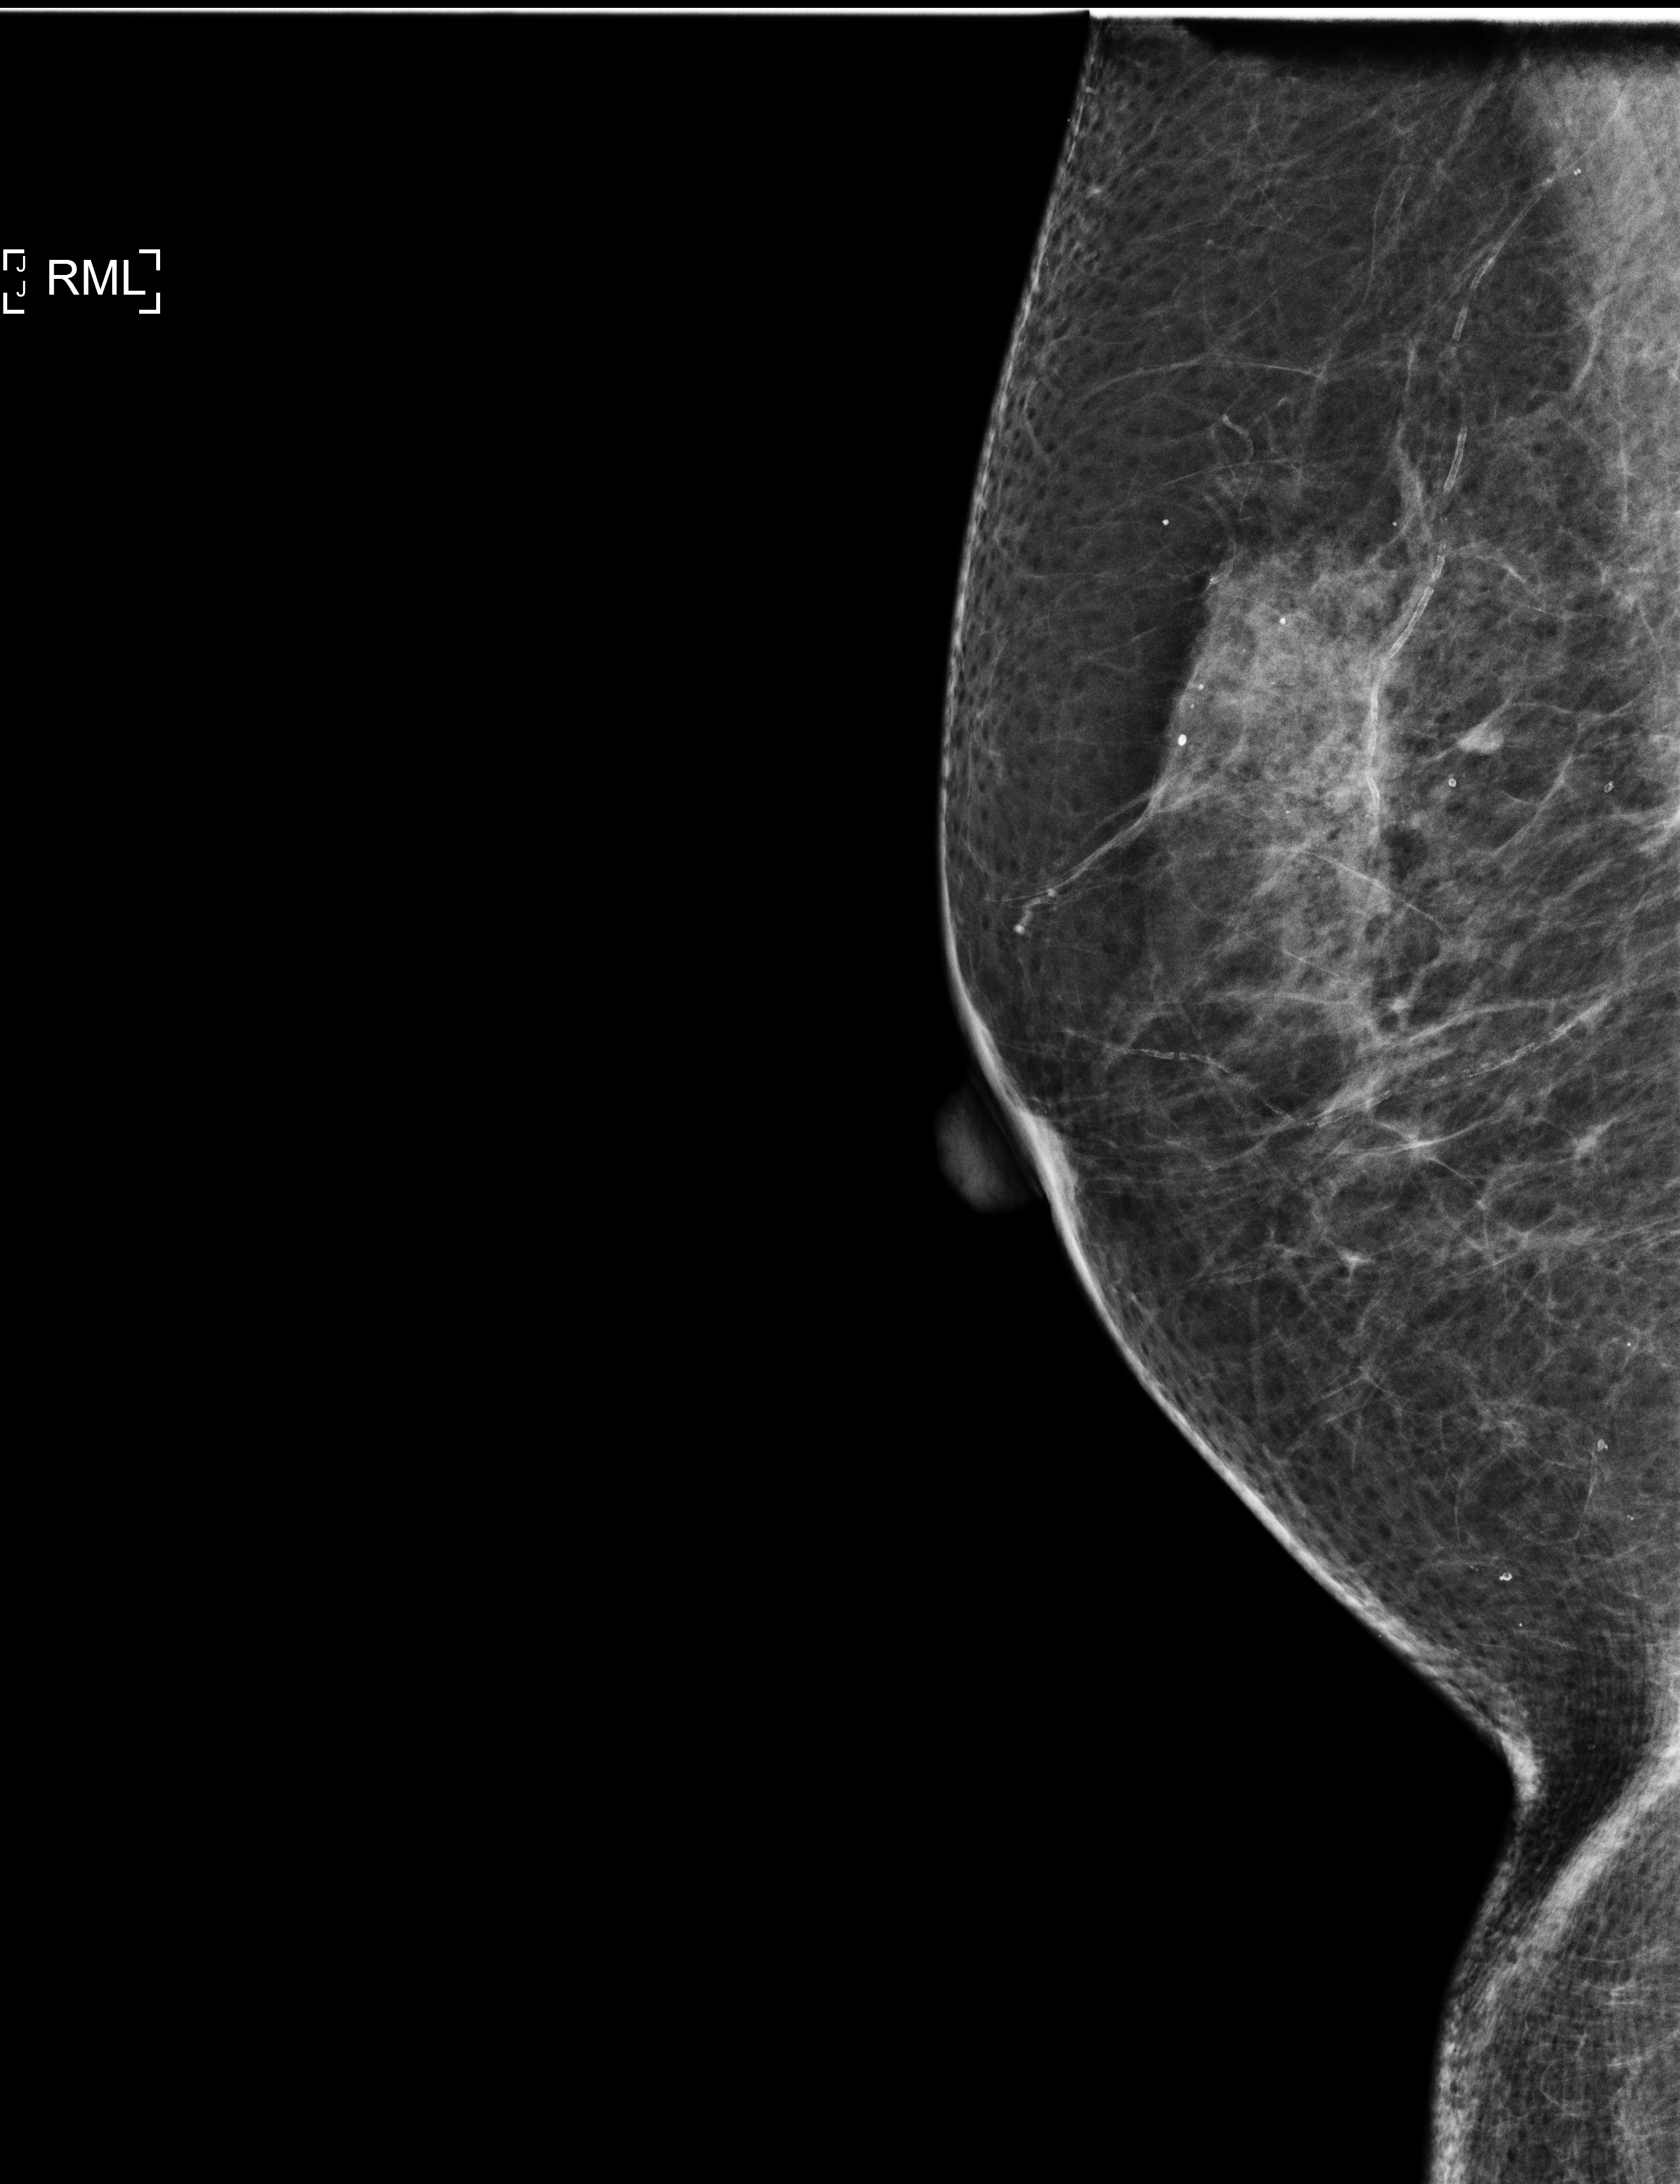
Diagnostic examination (additional views); compressed breast thickness 82 mm; system: Selenia Dimensions. Female patient, age 68 years.
Image type: full-field digital mammogram. Breast: right. Projection: mediolateral (ML) view.